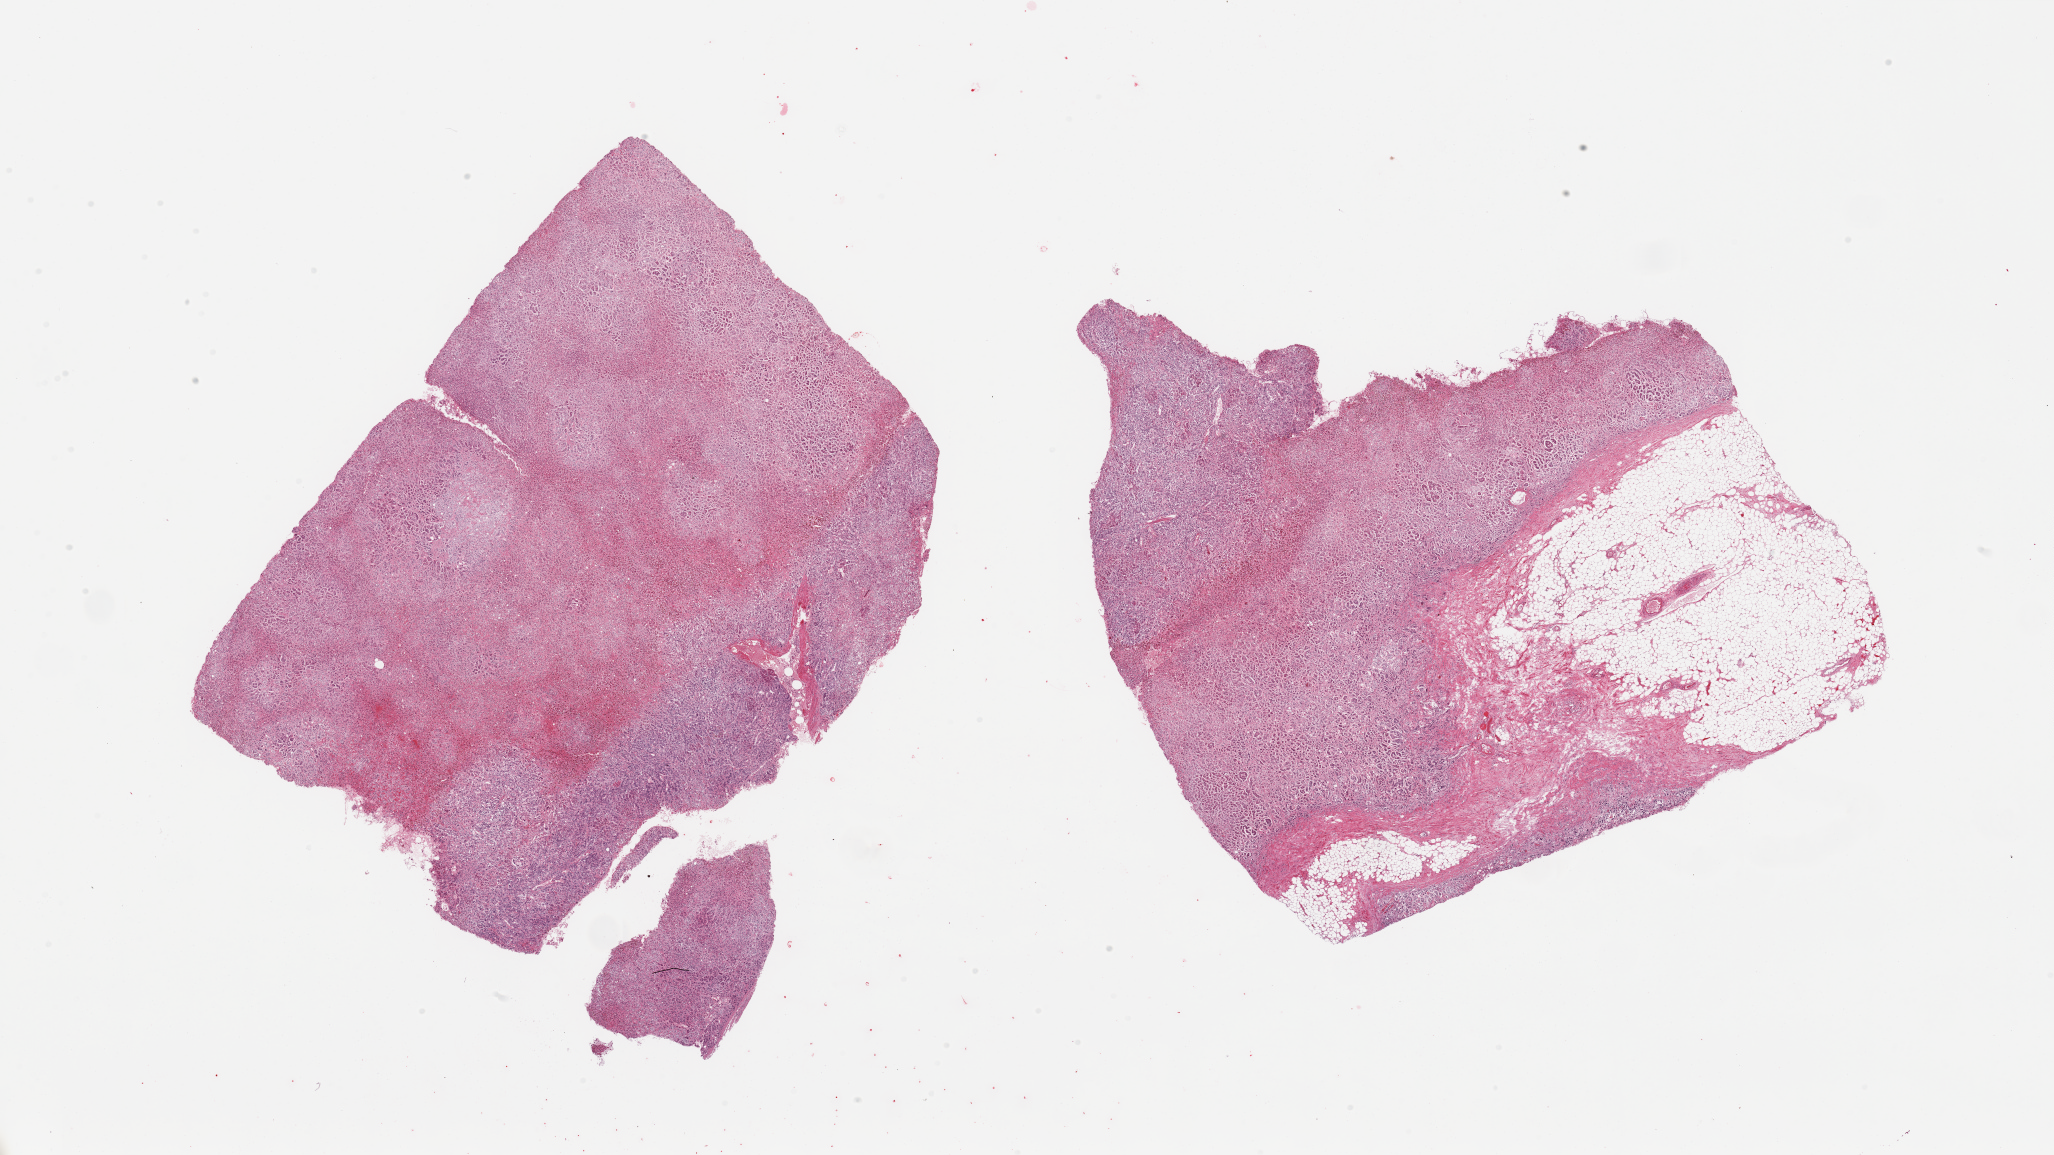
Whole-slide image, hematoxylin and eosin (H&E) stain — low-resolution overview of the scanned area, about 32.5 x 18.3 mm; PAXgene-fixed, paraffin-embedded tissue; target tissue: adrenal gland; donor tissue sample.
Review note (as recorded): 2 pieces; 1 piece is ~30% fat, hemorrhage, ~15-20% of the specimen is medulla.